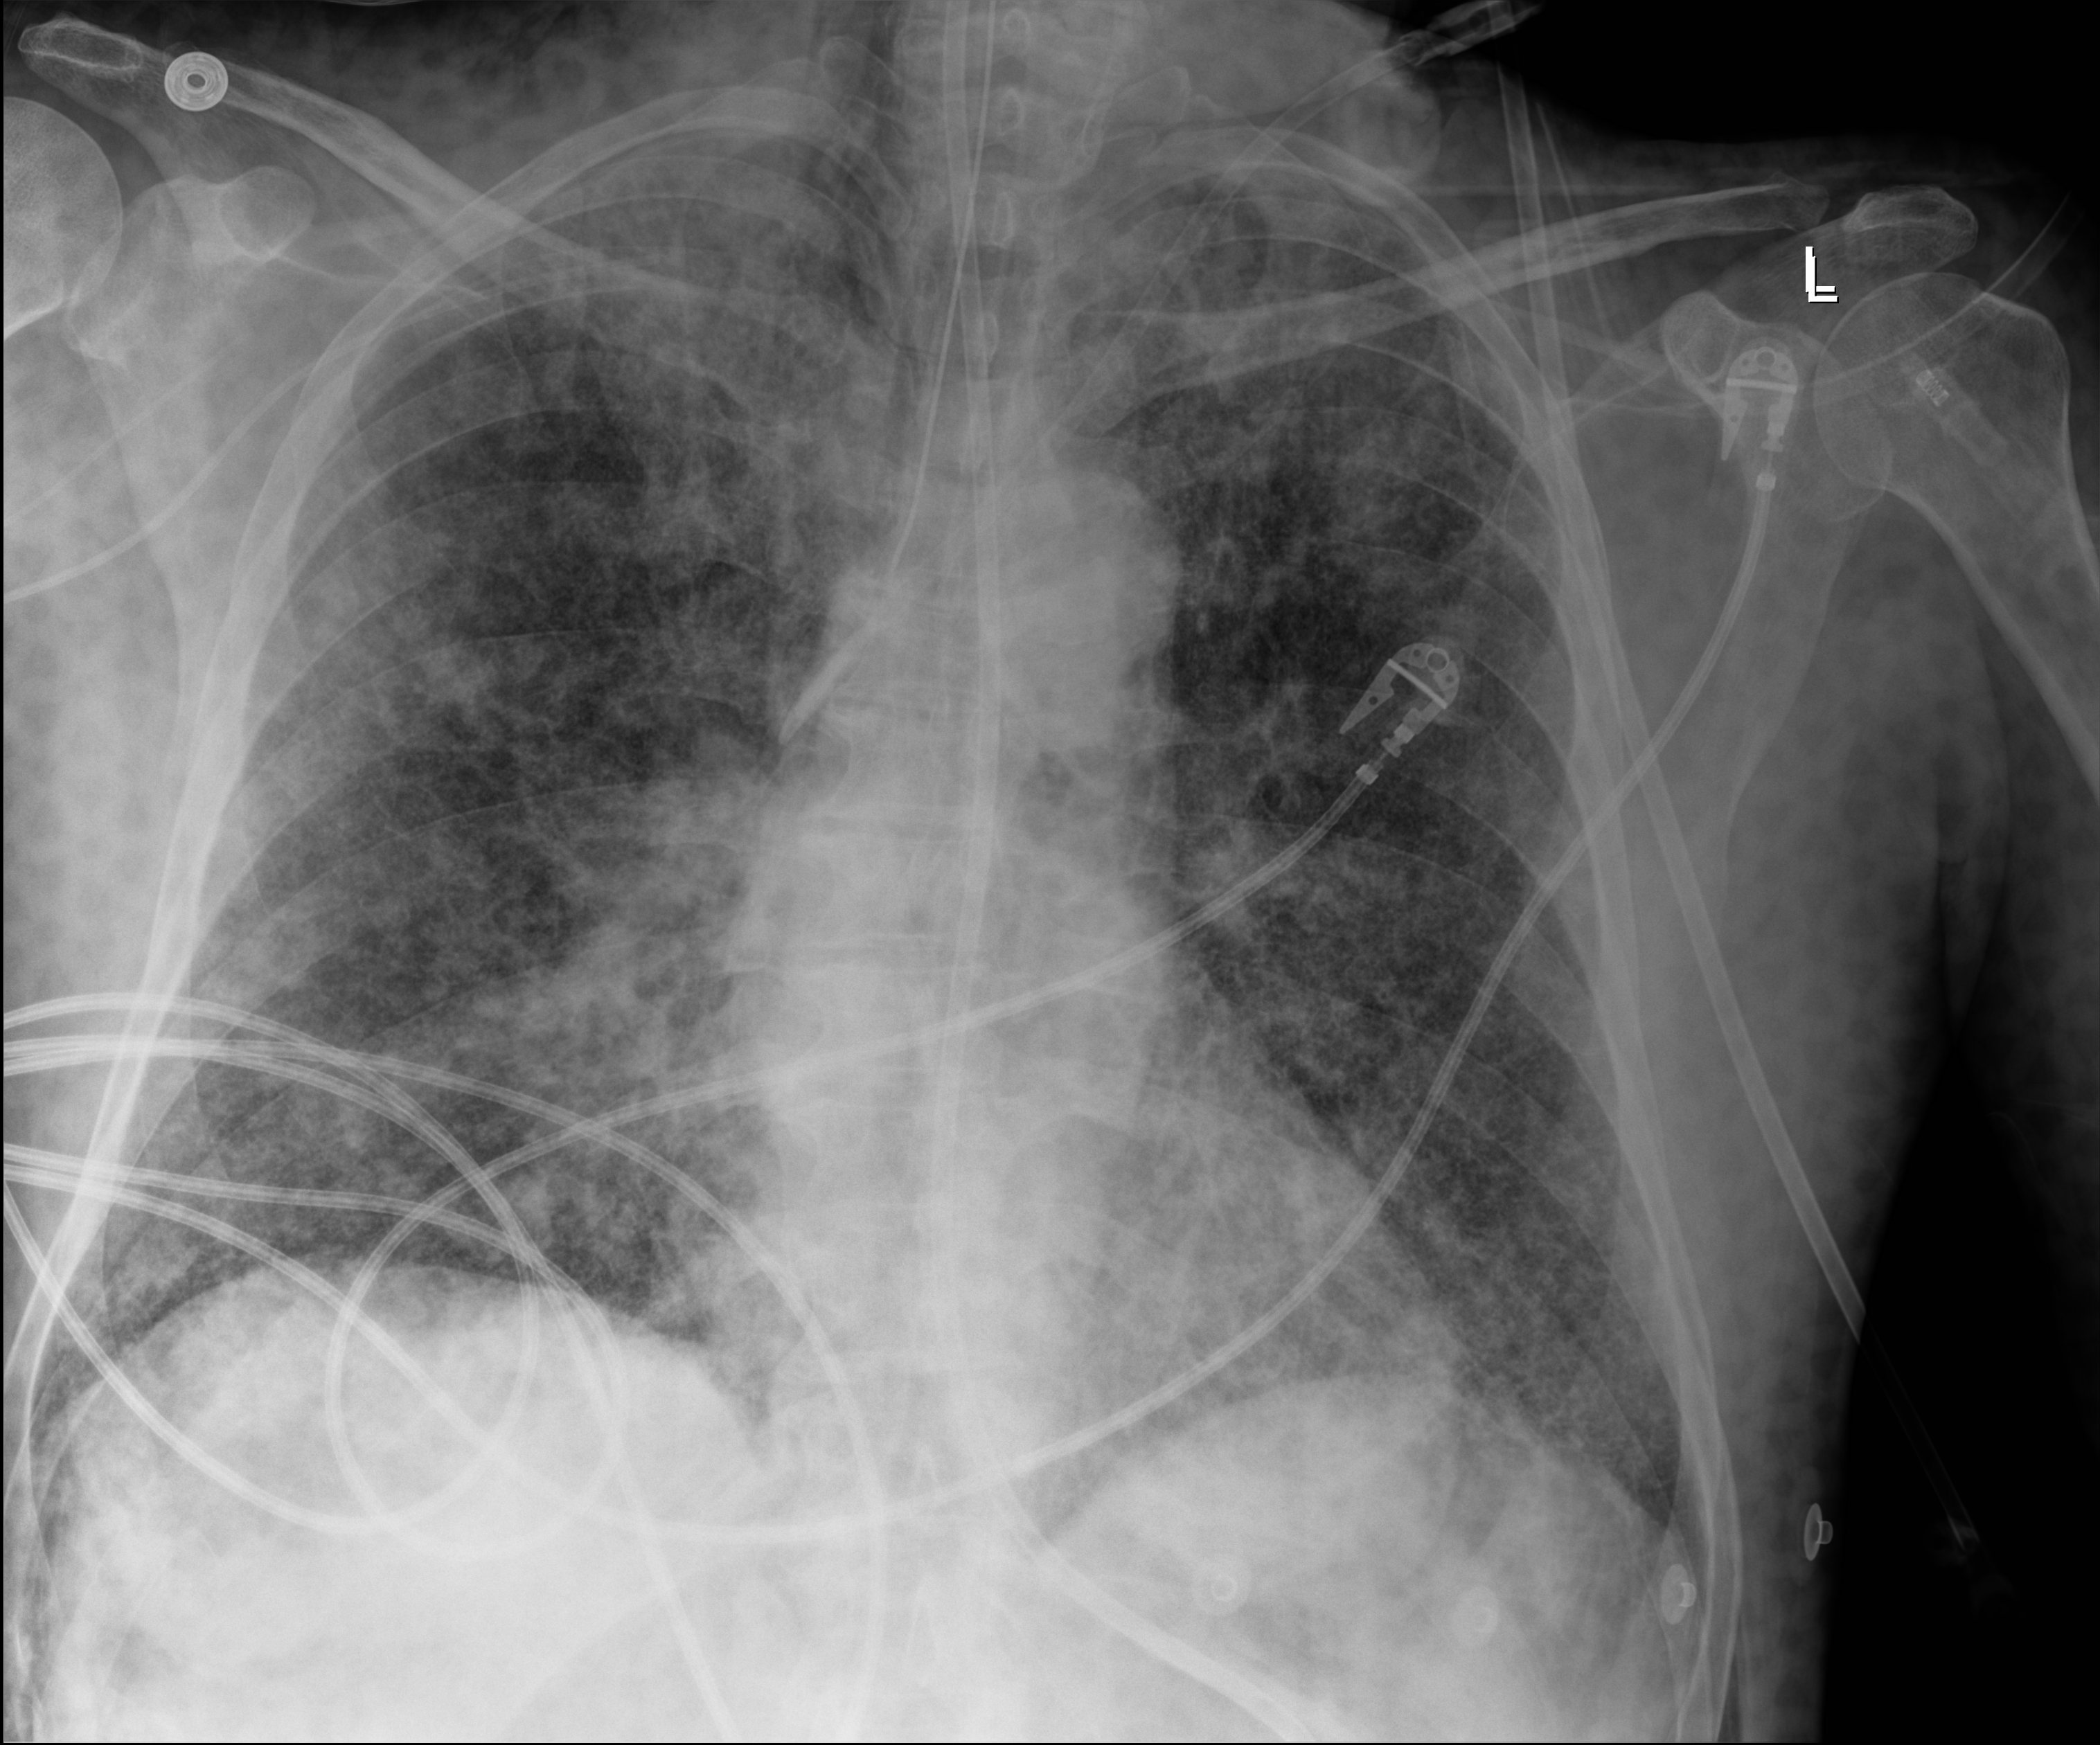
Portable chest radiograph; anteroposterior (AP) projection. Male patient hospitalised with COVID-19, age 18–59 years.
Admission-level facts for this patient (not findings on this image; timing relative to this image not recorded): admitted to intensive care during this hospital stay: yes.